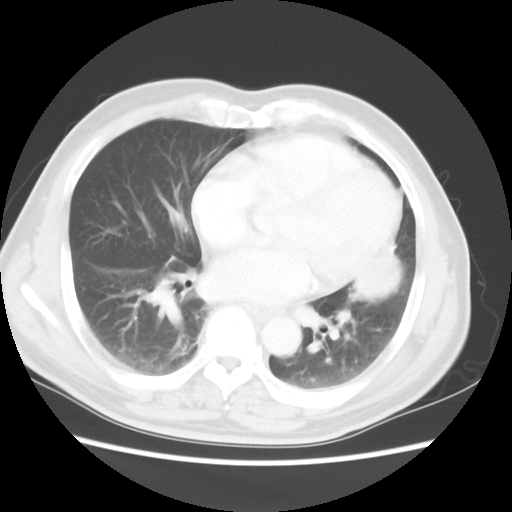
Chest CT, one axial slice; slice 21 of 50 in the series (ordered by position); 120 kVp; lung window (W 1500 / L -600 HU); 5 mm slice thickness; 512 × 512 image matrix, field of view 360 × 360 mm. Patient: male, 69 years. Case-level facts recorded for this patient, not image findings: clinical TNM (as recorded): T3 N1 M1a.
Outlined on this slice (rectangle marked by the reading radiologist):
- lung tumour (recorded histology: squamous cell carcinoma): bounding box (x1, y1, x2, y2) in pixels: (346, 231, 410, 315)